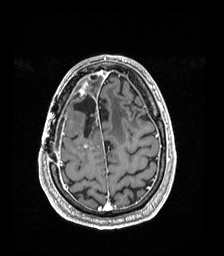
Brain MRI from a brain-tumour surgery series, one axial slice. Position 44 of 192 along the scan axis. T1-weighted post-contrast. 1 mm slice thickness. 224 × 256 image matrix, field of view 224 × 256 mm. From the clinical record (not read from this slice): histopathology: Astrocytoma; WHO grade: 4; IDH mutation: yes; tumour location: Right Frontal.
Annotated regions visible in this slice (expert manual segmentation):
- previous resection cavity: bounding box [x1, y1, x2, y2] px = [73, 95, 96, 137]
- tumour: [79, 81, 89, 97]